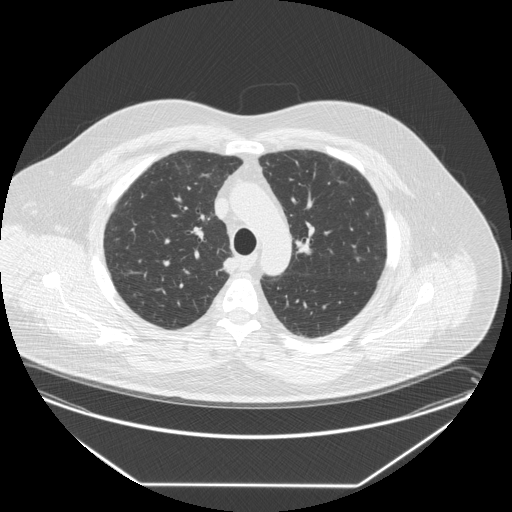
Low-dose screening chest CT, one axial slice. Slice 198 of 258 in the series (ordered by position). Lung window (W 1500 / L -600 HU). 2.5 mm slice thickness. 512 × 512 image matrix, field of view 440 × 440 mm.
Structures marked on this image (expert manual segmentation):
- lesion 1 (tumor, upper lobe of right lung): bounding box <220,257,238,276> (left, top, right, bottom; pixels)